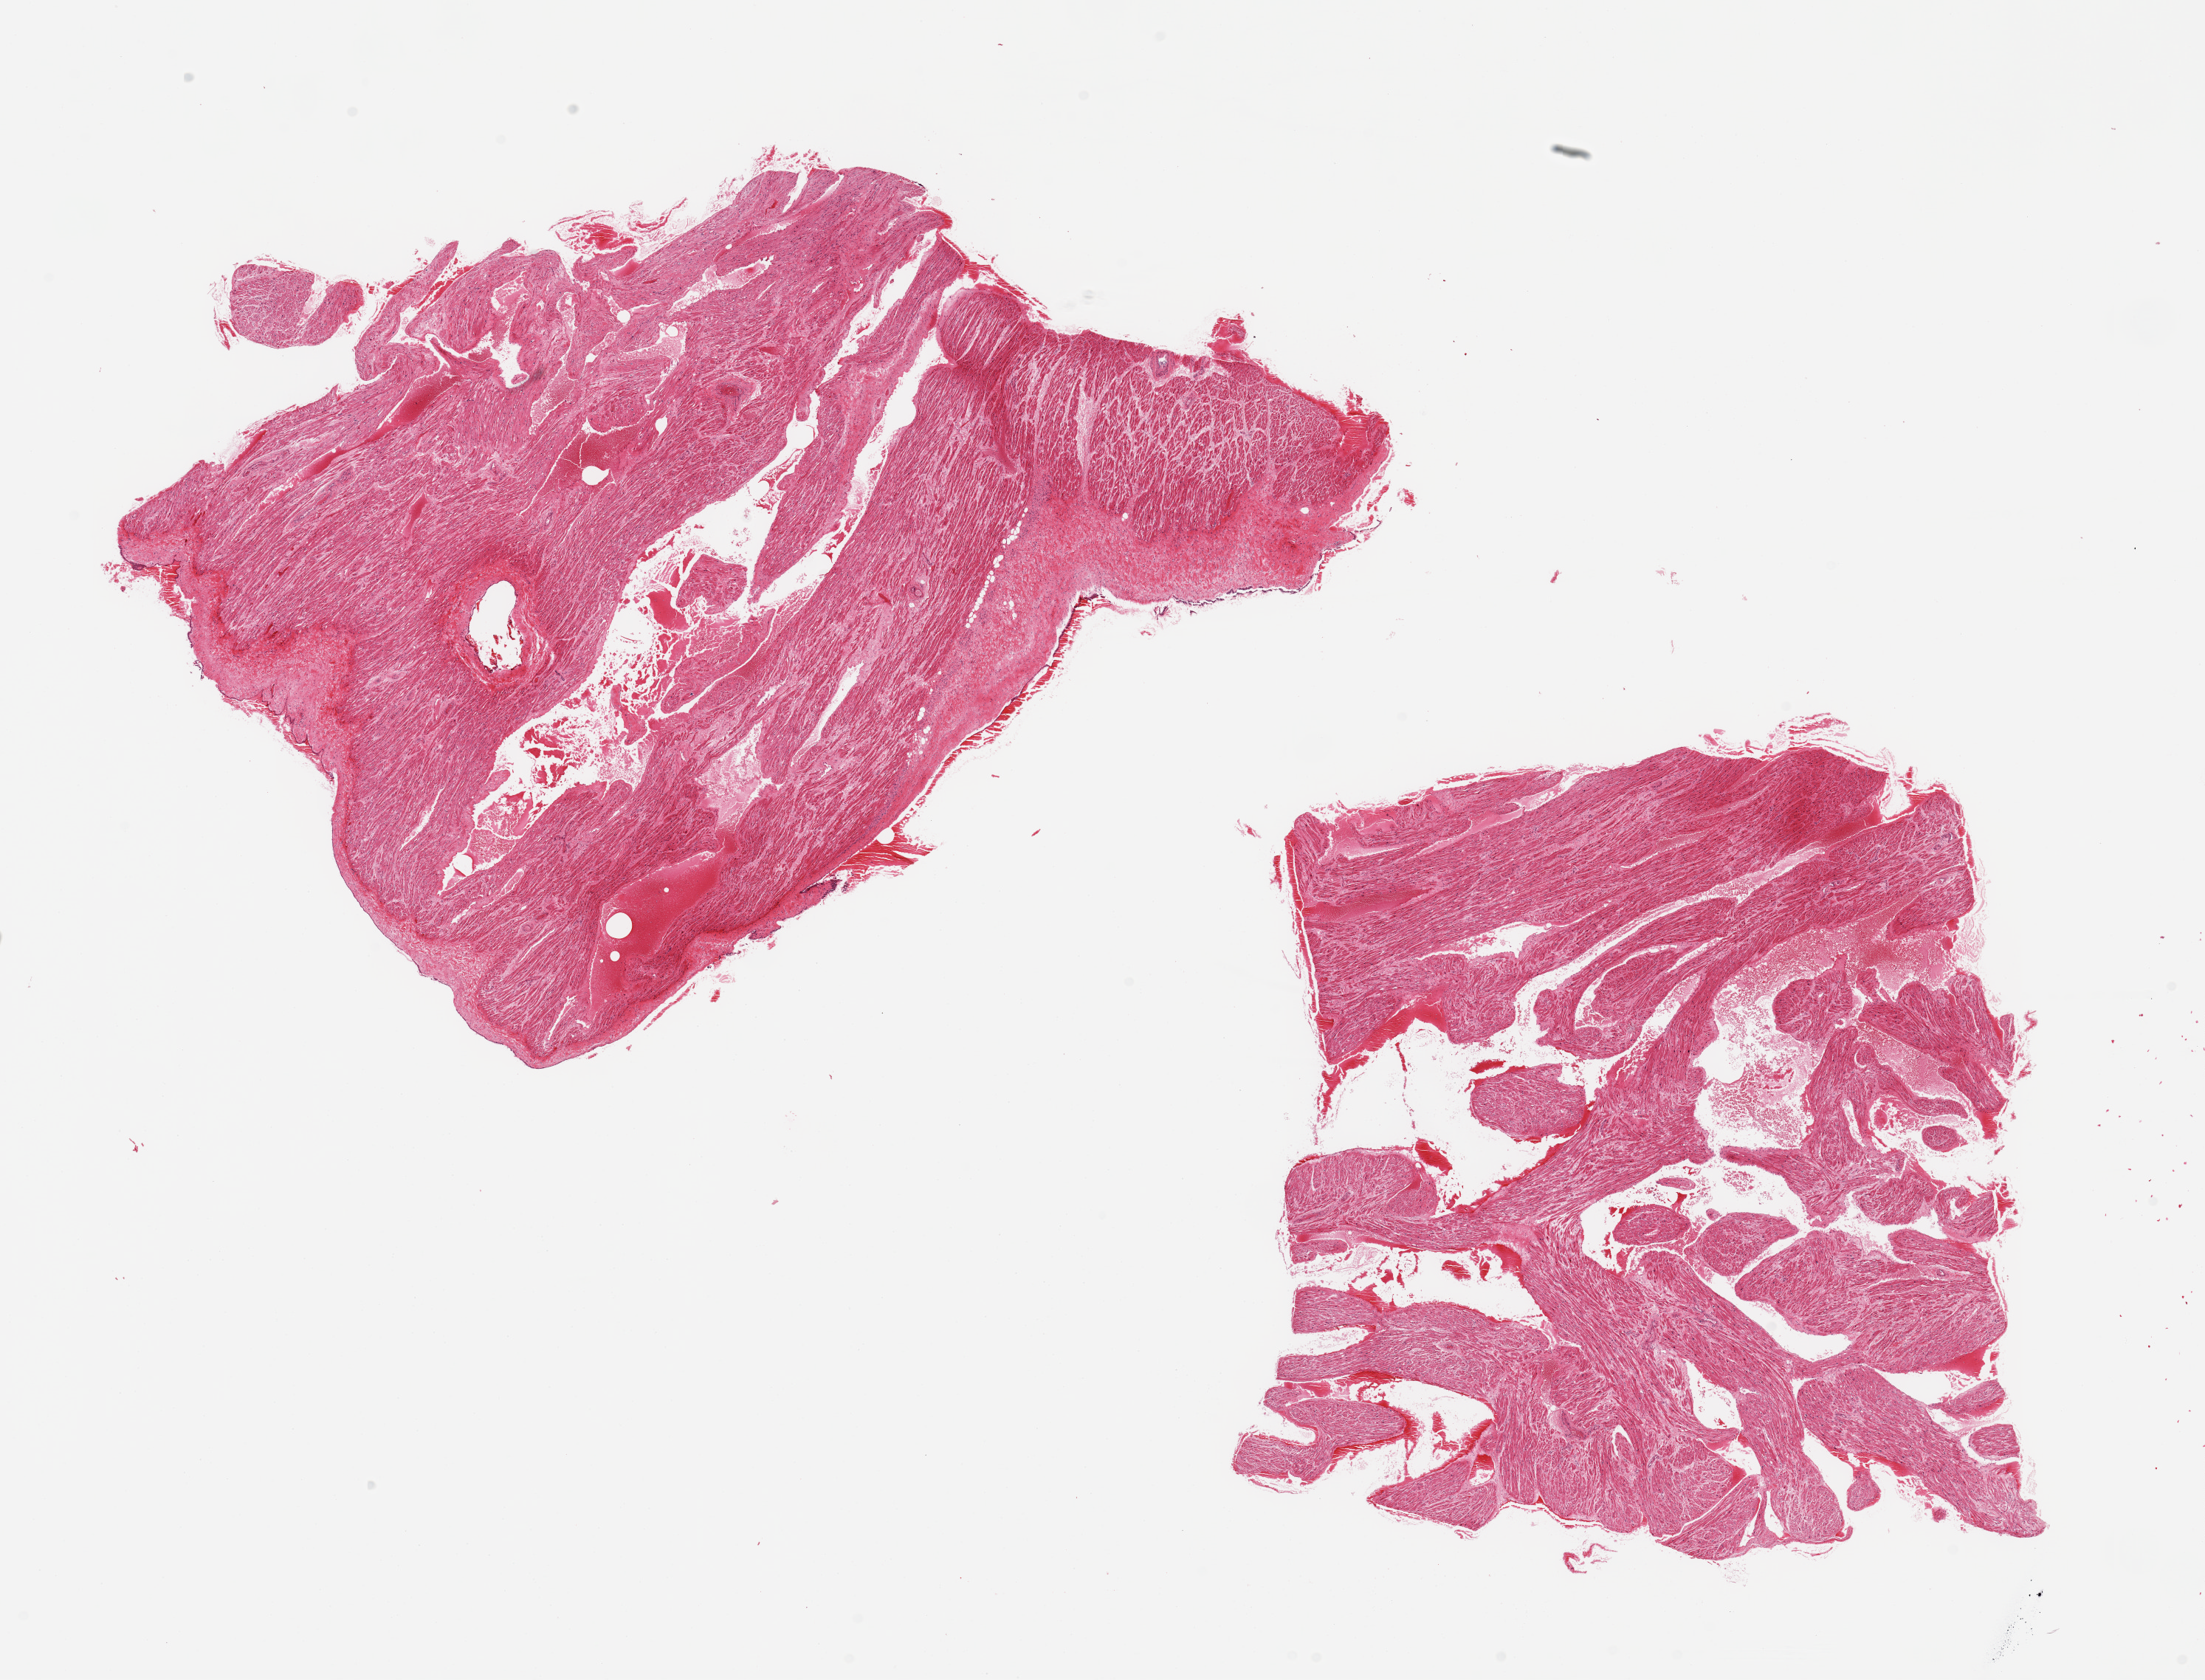
Whole-slide image, haematoxylin and eosin stain, a low-resolution overview of the entire scanned area, about 23.6 x 18.0 mm (slide scanned at 20x). PAXgene-fixed paraffin-embedded (PFPE) section. Section of auricular appendage (target tissue). Donor tissue sample. Donor sex: male.
* reviewer comment on this tissue sample: 2 pieces, no abnormalities